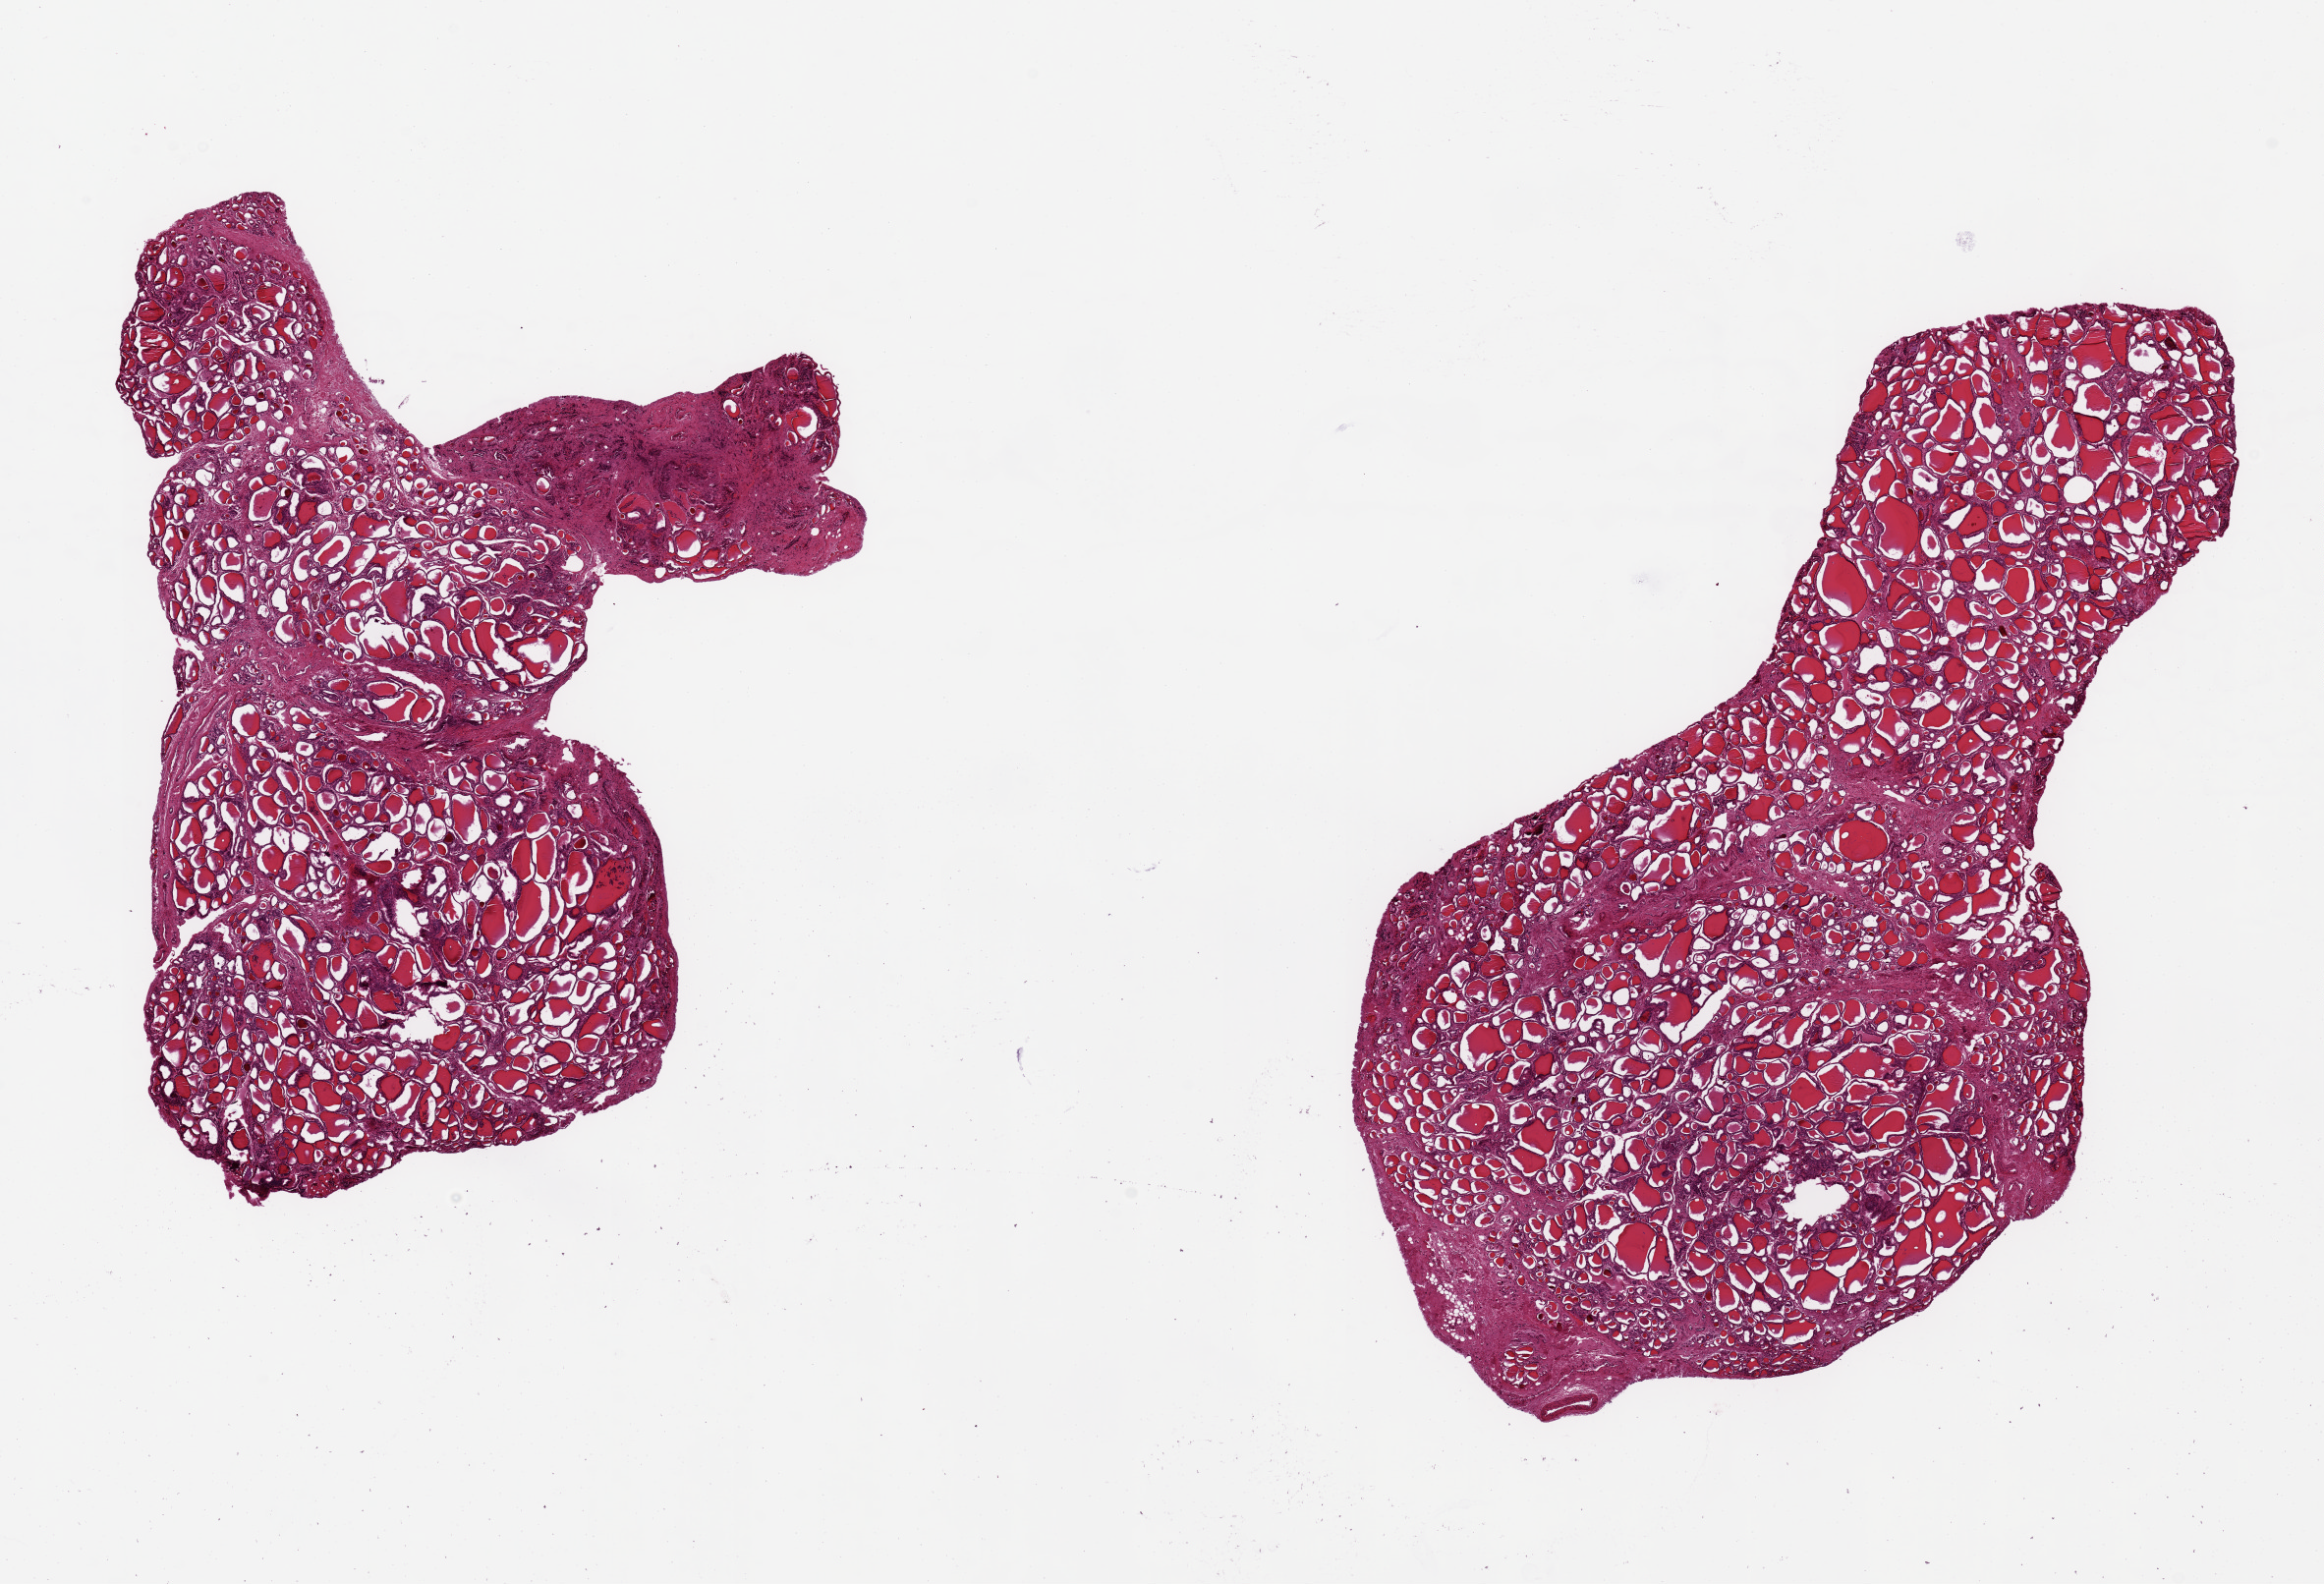
H&E whole-slide image, brightfield — shown as a low-resolution overview of the whole scanned area (about 18.7 x 12.7 mm, acquisition: 20x scan), PAXgene-fixed paraffin-embedded (PFPE) section, section of thyroid (target tissue), tissue donor sample. Donor: female.
Review note (as recorded): 2 pieces 10x5 & 8x4 mm; 2.5x1.7 mm fibrosed projection on smaller piece.